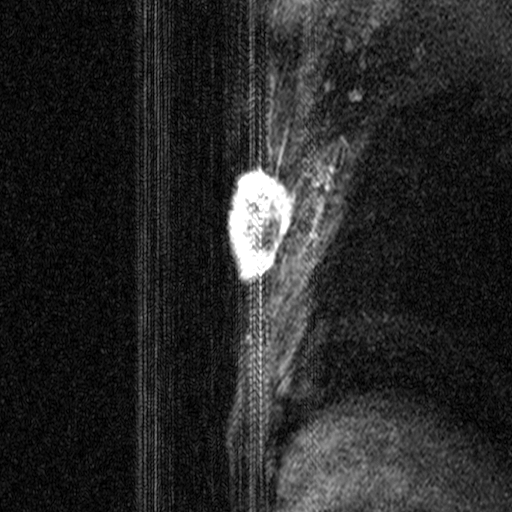
Breast MRI (dynamic contrast-enhanced), one sagittal slice. Position 29 of 44 along the scan axis. Dynamic contrast-enhanced study with each time point stored as its own series, time point 2 of 3 at this slice position (early post-contrast, ordered by acquisition time). 1.5 T. TE 4.5 ms, TR 11 ms. 3 mm slice thickness. 512 × 512 image matrix, field of view 200 × 200 mm. Female patient, age 44 years. From the clinical record (not read from this slice): setting: breast cancer imaged before/during neoadjuvant chemotherapy; receptor status: HR-positive, HER2-negative.
Annotated regions visible in this slice (semi-automatic segmentation, software-assisted and operator-edited):
- analysis volume of interest (the breast-tissue region the enhancement analysis was run in; not a lesion): box from (x=206, y=164) to (x=299, y=299) px
- tumour enhancement mask (voxels above the 90 % enhancement threshold inside the analysis volume of interest): (x=229, y=165)–(x=296, y=275)